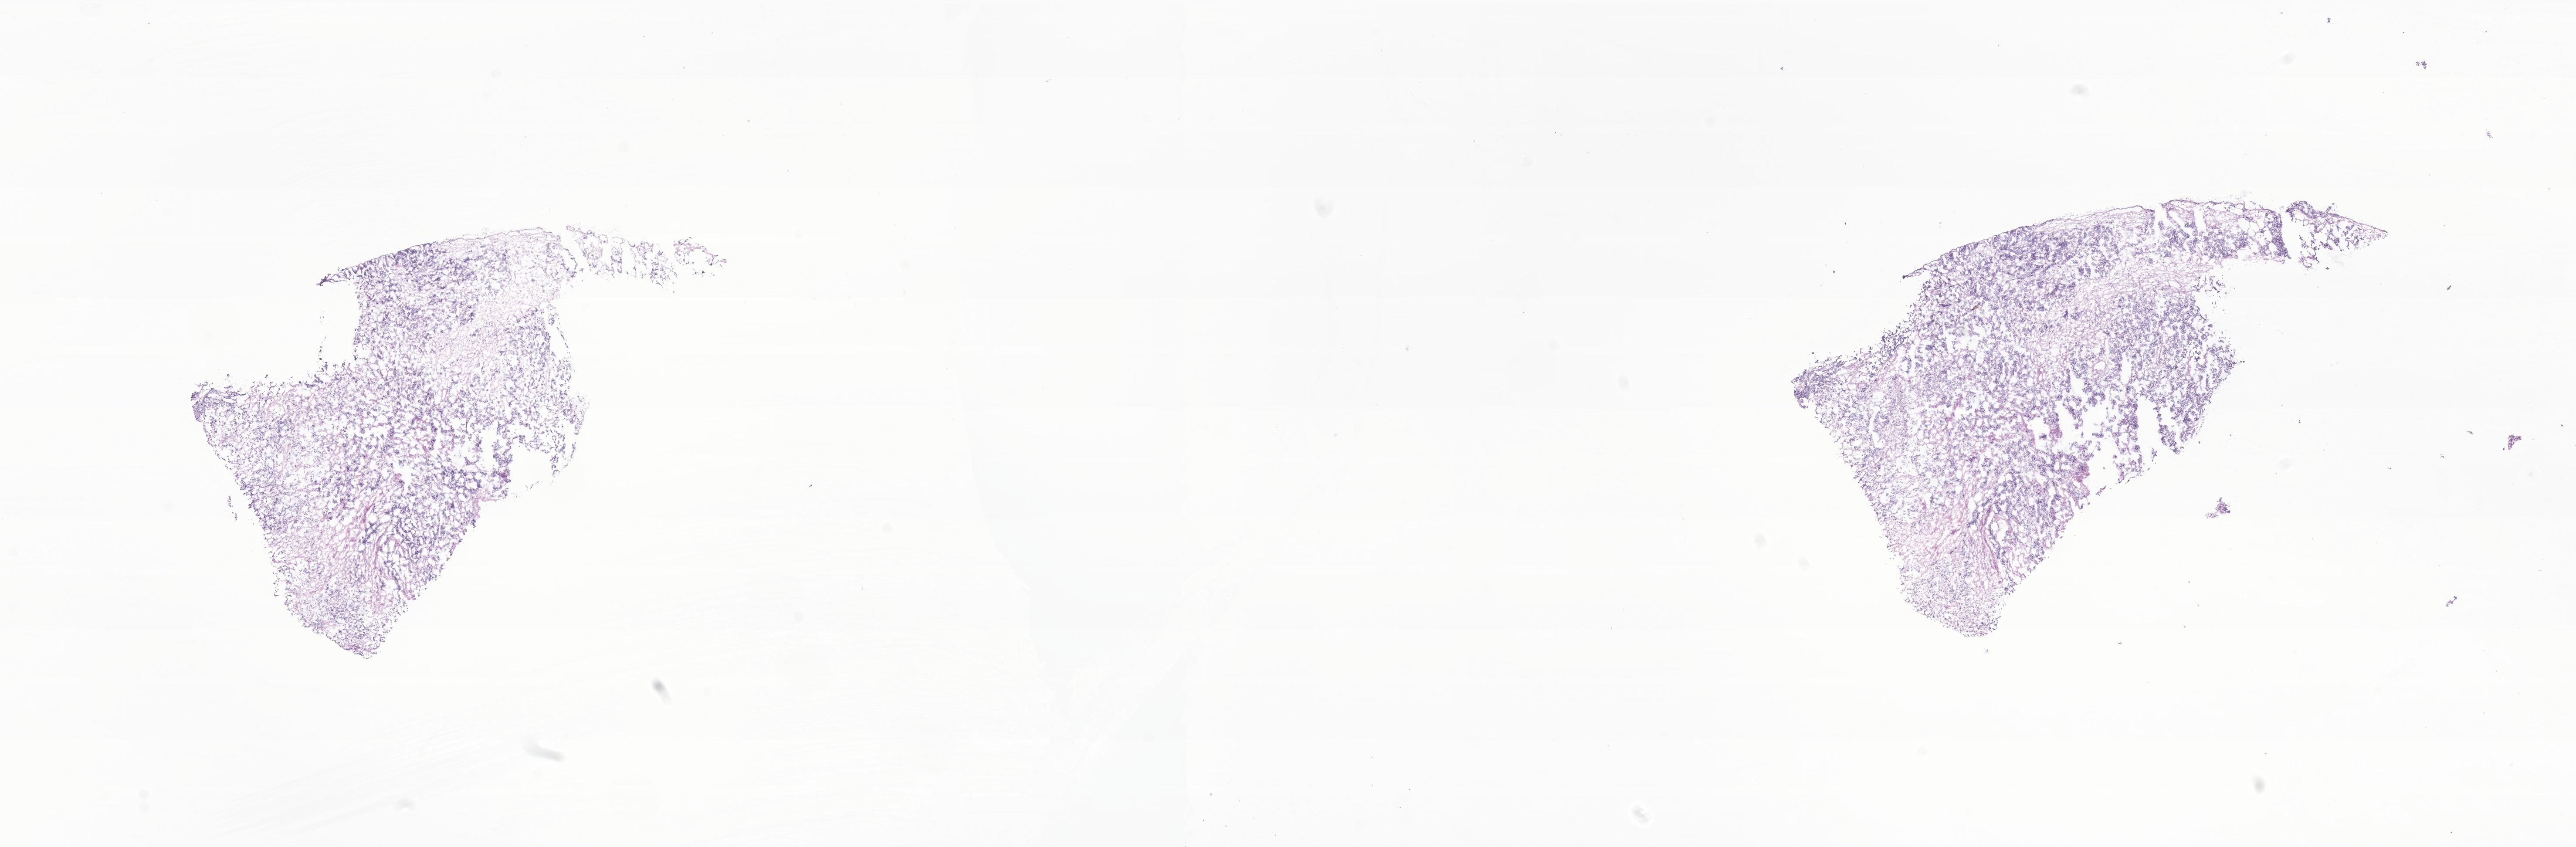
Whole-slide image, H&E stain of tumor tissue from the retroperitoneum, low-resolution overview of the scanned area, about 24.9 x 8.2 mm; frozen section (OCT-embedded). Male patient, age 34 months (2 years 10 months).
Recorded diagnosis: Neuroblastoma, NOS.